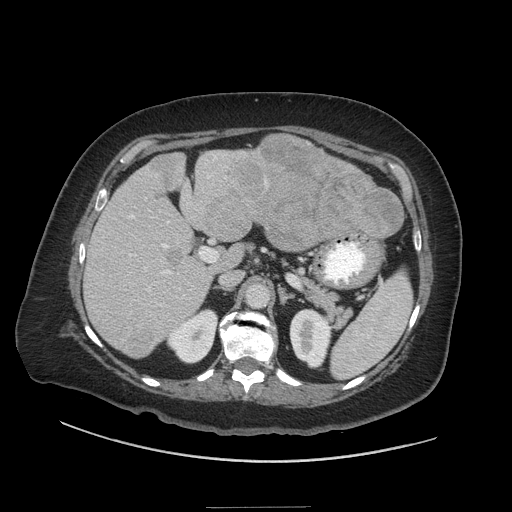
Contrast-enhanced abdominal CT (liver protocol), one axial slice. Position 22 of 81 along the scan axis. Soft-tissue window (W 400 / L 40 HU). 512 × 512 image matrix, field of view 440 × 440 mm. Case-level facts recorded for this patient, not image findings: diagnosis: hepatocellular carcinoma (patient treated with transarterial chemoembolisation; whether this scan precedes or follows treatment is not stated here); TNM stage (as recorded): Stage-II; Child-Pugh class: A; tumour differentiation: moderately differentiated.
Outlined on this slice (semi-automatically segmented with operator editing):
- liver parenchyma outside the tumour (the mass and vessels are separate outlines, so this box may not span the whole liver): bounding box <84,136,404,358> (left, top, right, bottom; pixels)
- mass: <129,136,402,356>
- liver vessels: <129,175,213,306>